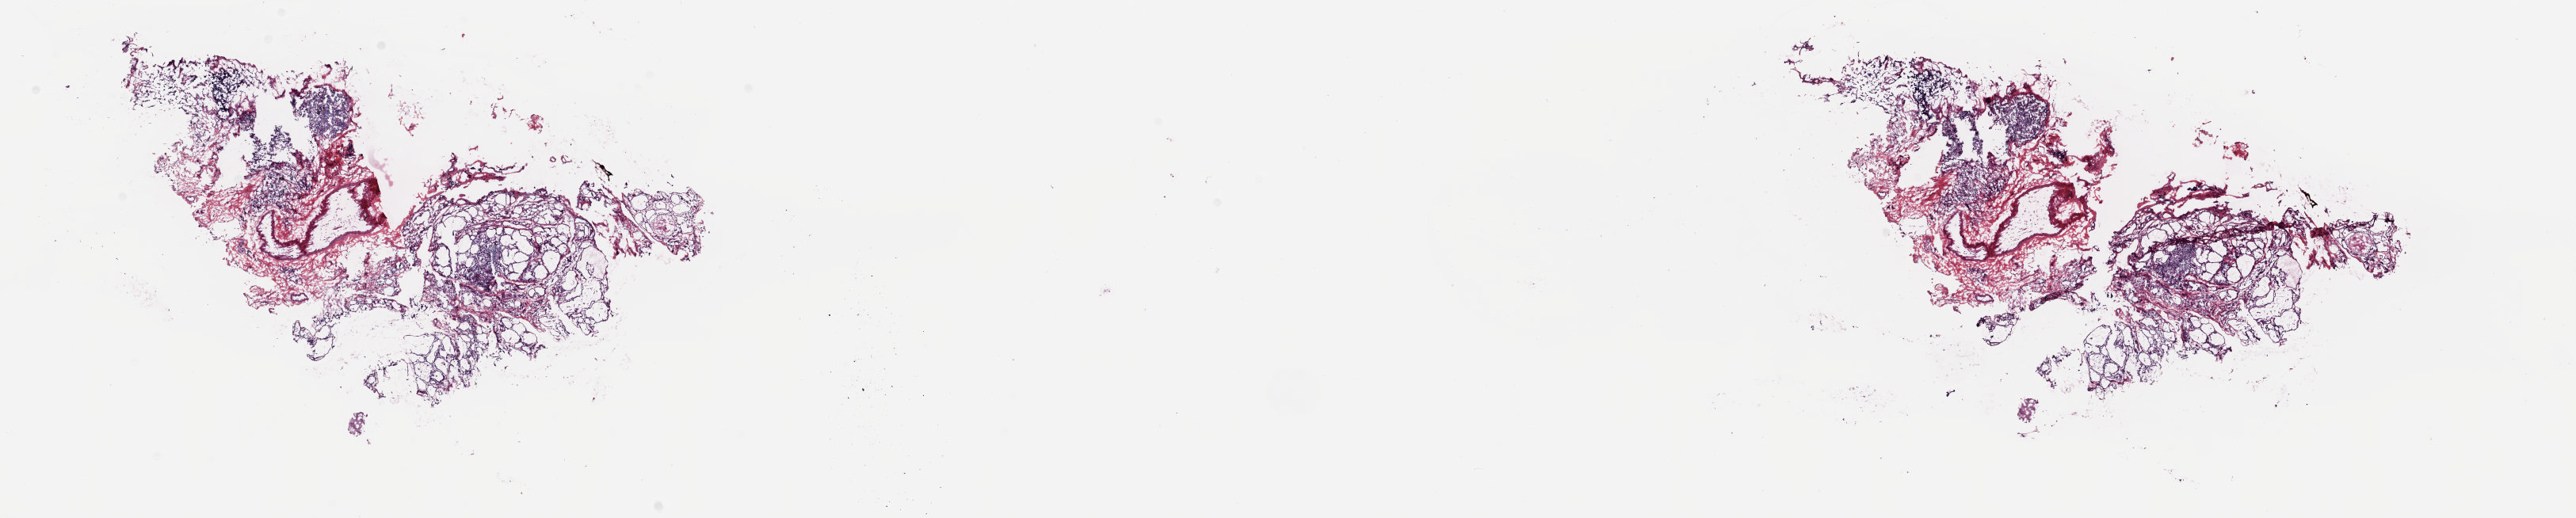
Whole-slide histology image, Hematoxylin and eosin (H&E) stained, low-resolution overview of the scanned area, about 25.8 x 5.2 mm, frozen section from the top of the tissue portion, solid tissue normal (non-tumour tissue) sample from the thyroid. Female, age 51 years at initial diagnosis. Slide review estimates, as recorded: tumour cells 0%, tumour nuclei 0%, normal cells 100%, stromal cells 0%, necrosis 0%. Infiltration values recorded for this section: lymphocyte infiltration 5%, monocyte infiltration 2%, neutrophil infiltration 0%.
• this section: solid tissue normal sample (biorepository sample class)
• patient diagnosis: Papillary carcinoma, columnar cell (thyroid gland)